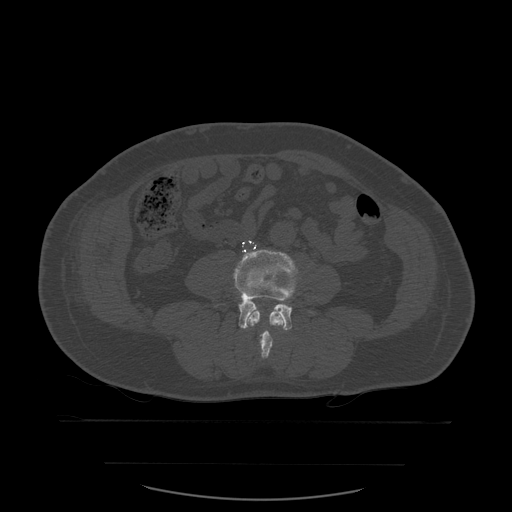
CT including the spine, one axial slice. Slice 175 of 590 in the series (ordered by position). Bone window (W 1800 / L 400 HU). 1.25 mm slice thickness. 512 × 512 image matrix. Patient age 71 years. Case-level facts recorded for this patient, not image findings: primary cancer: lung; vertebrae with lytic lesions (as recorded): T1, T2, L5, S1.
Structures marked on this image (semi-automatically segmented with operator editing):
- L3 vertebra: bounding box [x1, y1, x2, y2] px = [247, 311, 285, 359]
- L4 vertebra: [234, 250, 298, 331]